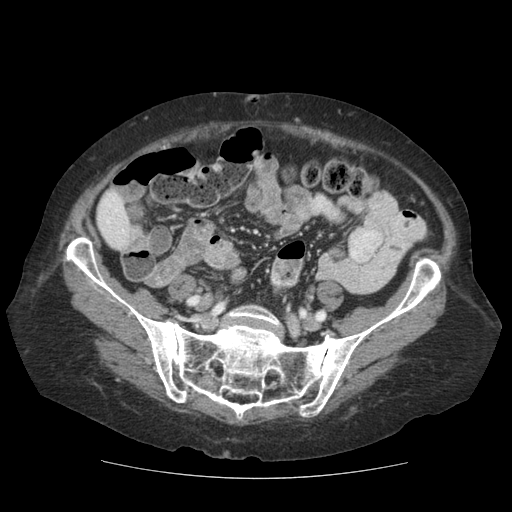
Contrast-enhanced abdominal CT (liver protocol), one axial slice; slice 14 of 111 in the series (ordered by position); reconstruction kernel STANDARD; soft-tissue window (W 400 / L 40 HU); 2.5 mm slice thickness; 512 × 512 image matrix, field of view 360 × 360 mm. From the clinical record (not read from this slice): diagnosis: hepatocellular carcinoma (patient treated with transarterial chemoembolisation; whether this scan precedes or follows treatment is not stated here); TNM stage (as recorded): Stage-I; Child-Pugh class: A; tumour differentiation: moderately-poorly differentiated; tumour nodularity: uninodular.
Outlined on this slice (semi-automatic segmentation, software-assisted and operator-edited):
- liver parenchyma outside the tumour (the mass and vessels are separate outlines, so this box may not span the whole liver): bounding box [x1, y1, x2, y2] px = [96, 190, 144, 250]
- liver vessels: [107, 210, 117, 223]